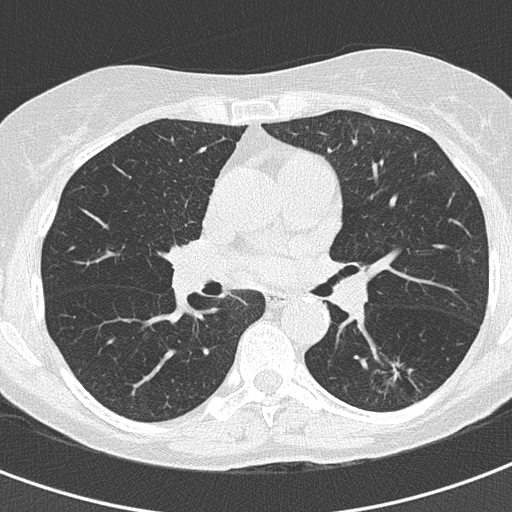
Low-dose screening chest CT, axial slice, second screening round (one year after baseline), lung window (W 1500 / L -600 HU), 2 mm slice thickness, lung (sharp) reconstruction kernel (B50f), slice 70 of 155 in the series. Female participant, aged 60 years at enrolment. Current smoker at enrolment.
• Lesion marked by an expert reader, bounding box [x1, y1, x2, y2] px = [377, 352, 419, 385].
• Screening reader's record for this exam (one nodule recorded; not confirmed to be the boxed lesion): non-calcified nodule or mass ≥4 mm, left lower lobe, 10 × 9 mm, soft tissue attenuation.
• Official screen result: positive, other.
• Later outcome: lung cancer diagnosed 64 days after this screen — adenocarcinoma, NOS, left lower lobe, well differentiated (G1), stage IA (AJCC 6th edition), 15 mm at pathology.